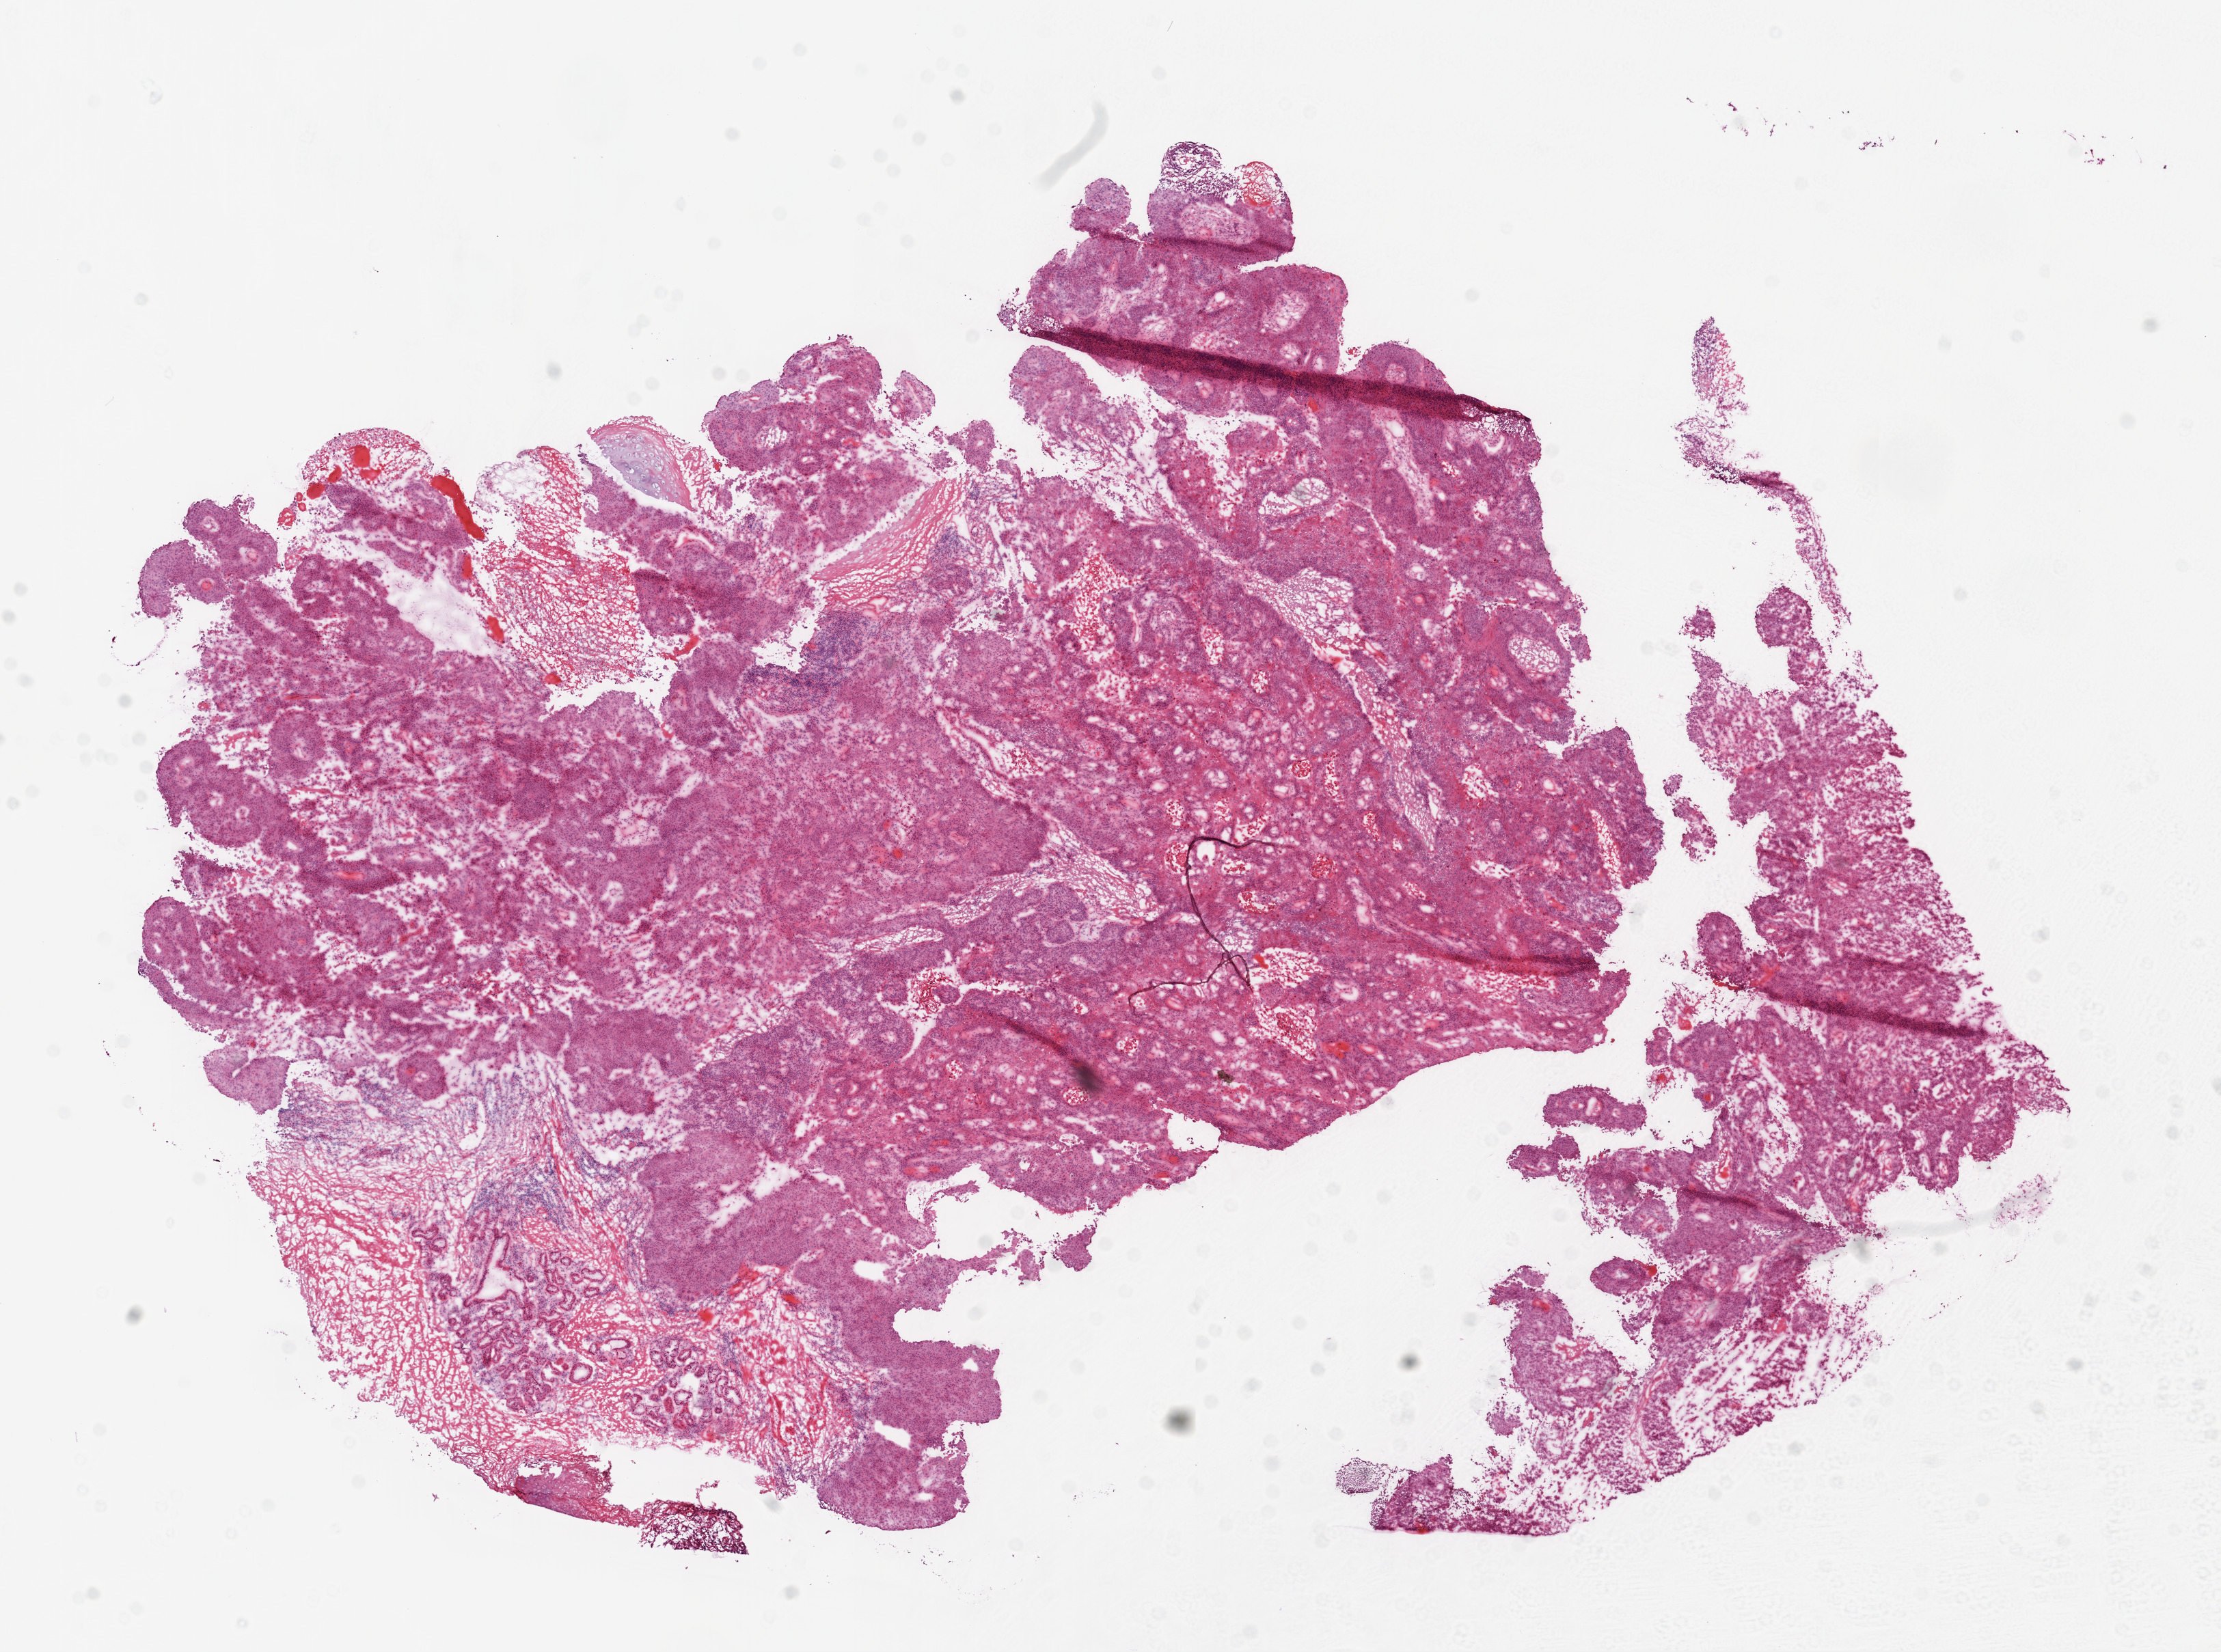
Whole-slide histology image, Hematoxylin and eosin (H&E) stained — whole scanned area (about 13.0 x 9.7 mm) shown as a low-resolution overview. Frozen section from the top of the tissue portion. Lung, primary tumour sample. Male patient; age at initial diagnosis 74 years. Pathologist review of this section (percent, as recorded): tumour cells 74%, tumour nuclei 80%, normal cells 13%, stromal cells 0%, necrosis 13%. Infiltration values recorded for this section: lymphocyte infiltration 10%, monocyte infiltration 1%, neutrophil infiltration 1%.
* AJCC pathologic stage: IA
* laterality: left
* diagnosis: Squamous cell carcinoma, NOS (lower lobe, lung)